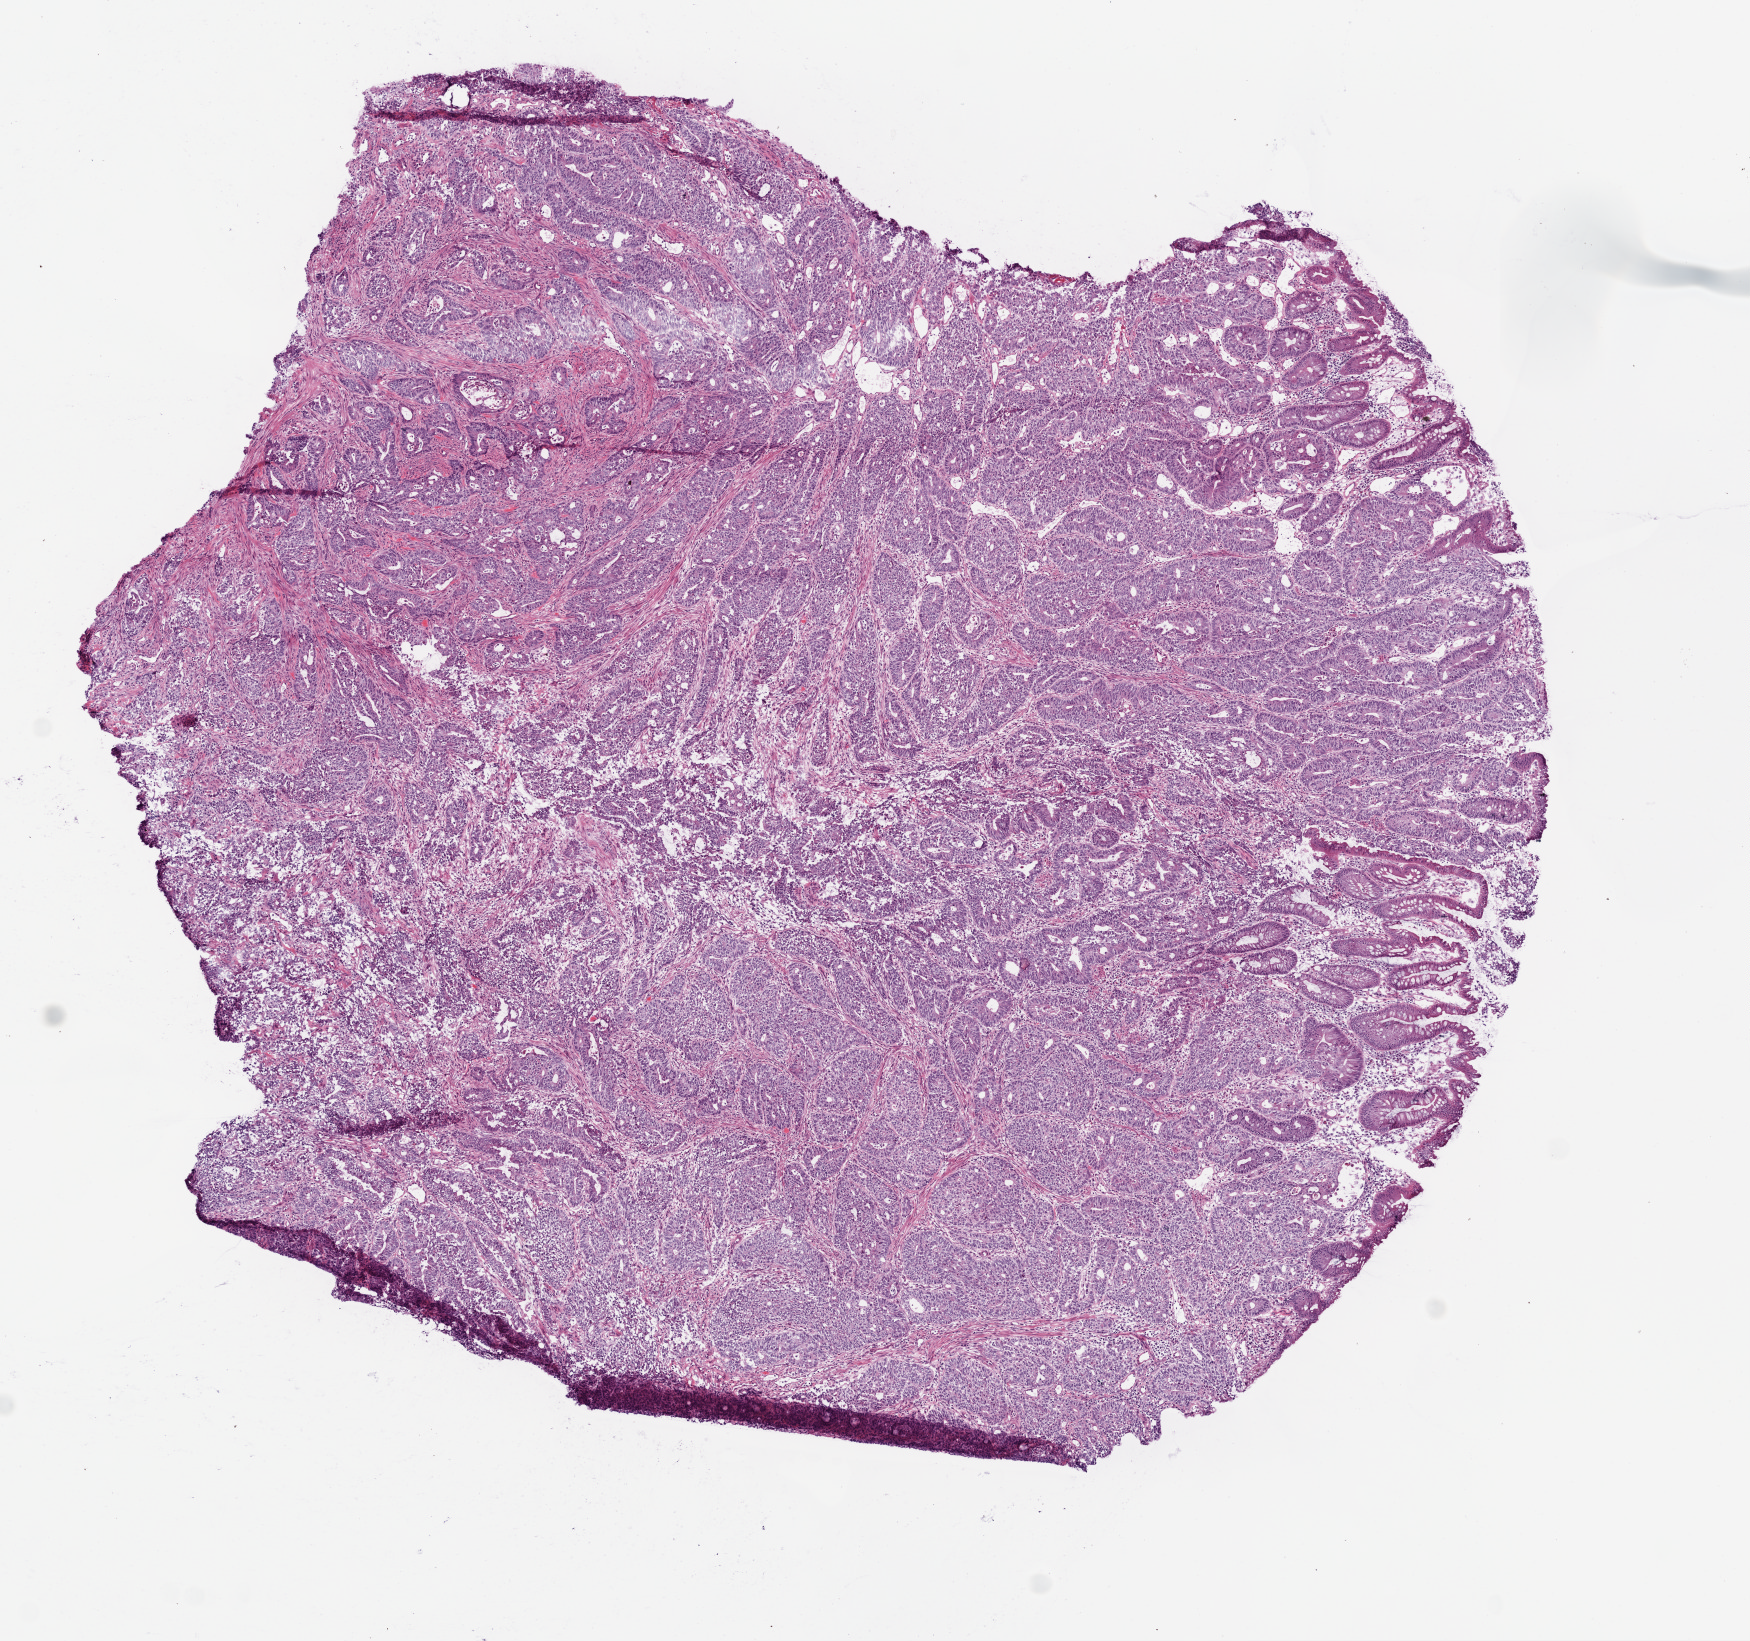
Whole-slide histology image, H&E-stained — shown as a low-resolution overview of the whole scanned area (about 7.0 x 6.6 mm); frozen section; primary tumour sample from the colon. Female, age 86 years at initial diagnosis.
Pathologic diagnosis: Adenocarcinoma, NOS.